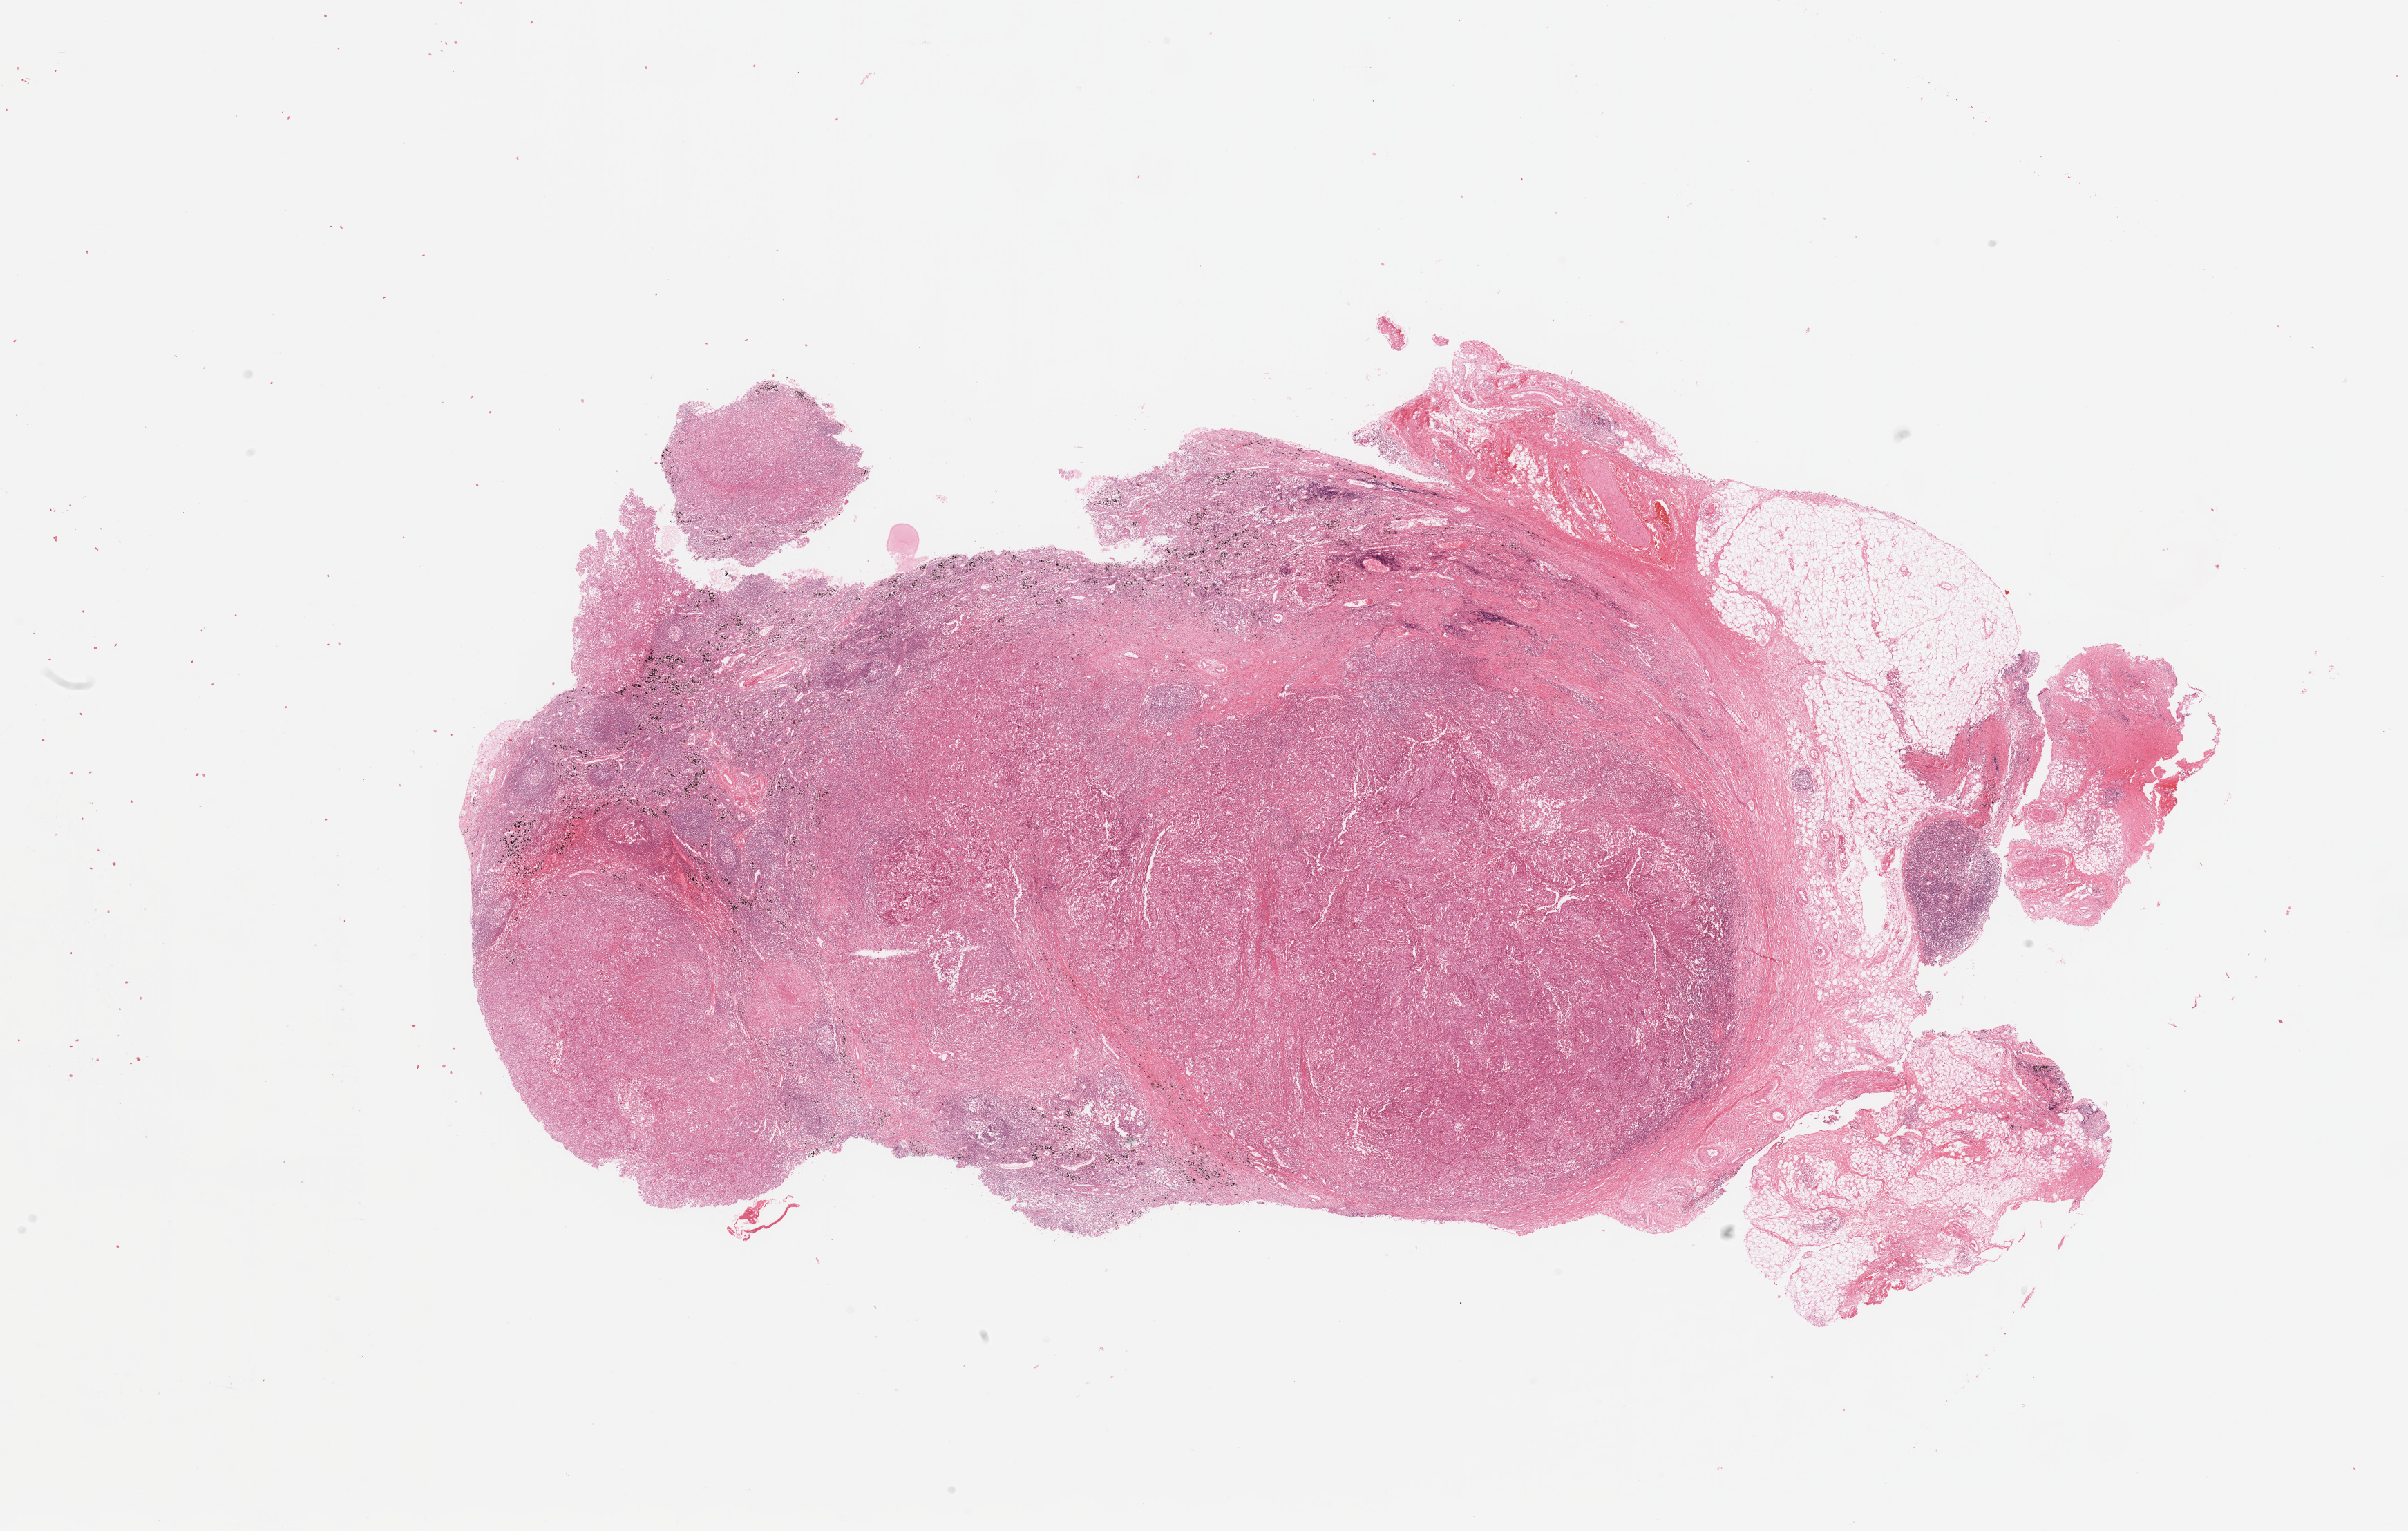
Whole-slide histology image, H&E-stained — whole scanned area (about 27.6 x 17.5 mm) shown as a low-resolution overview, tumour tissue sample, sampled site: lung. 54-year-old male patient. Composition of this section per pathologist review: tumour nuclei 65%, necrosis 5%.
Histologic diagnosis: Adenocarcinoma, NOS.